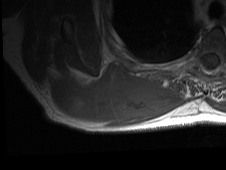
MRI of an extremity soft-tissue mass, one axial slice. Position 26 of 81 along the scan axis. MR volume resampled by the dataset authors to the PET/CT grid (not the native acquisition matrix). 3.27 mm slice thickness. 226 × 170 image matrix, field of view 221 × 166 mm. Male patient. From the clinical record (not read from this slice): histological type: pleiomorphic spindle cell undifferentiated; grade: high; site of the primary tumour: right parascapusular.
Outlined on this slice (expert contour drawn on MRI and transferred to this co-registered scan by the dataset authors):
- gross tumour volume including surrounding oedema: bounding box (x1, y1, x2, y2) in pixels: (46, 63, 184, 126)
- gross tumour volume (mass): (51, 65, 164, 123)